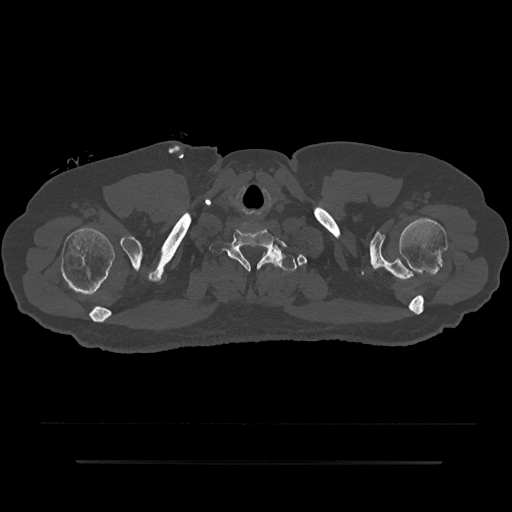
CT including the spine, one axial slice. Reconstruction kernel Br40s/3. 120 kVp. Bone window (W 1800 / L 400 HU). 512 × 512 image matrix, field of view 464 × 464 mm. Male patient, age 59 years. From the clinical record (not read from this slice): primary cancer: bile ducts; vertebrae with lytic lesions (as recorded): T10.
Outlined on this slice (semi-automatically segmented with operator editing):
- T1 vertebra: bounding box <243,250,297,271> (left, top, right, bottom; pixels)